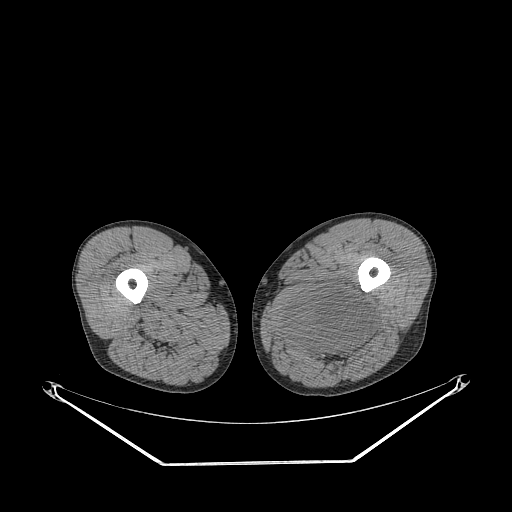
CT of an extremity soft-tissue mass (from a PET/CT study), one axial slice. Position 247 of 267 along the scan axis. Reconstruction kernel STANDARD. 140 kVp. Soft-tissue window (W 400 / L 40 HU). 3.75 mm slice thickness. 512 × 512 image matrix, field of view 500 × 500 mm. Male patient. From the clinical record (not read from this slice): histological type: undifferentiated pleomorphic liposarcoma; grade: high; site of the primary tumour: left thigh.
Annotated regions visible in this slice (expert contour drawn on MRI and transferred to this co-registered scan by the dataset authors):
- gross tumour volume including surrounding oedema: box from (x=278, y=288) to (x=375, y=360) px
- gross tumour volume (mass): (x=288, y=288)–(x=375, y=352)